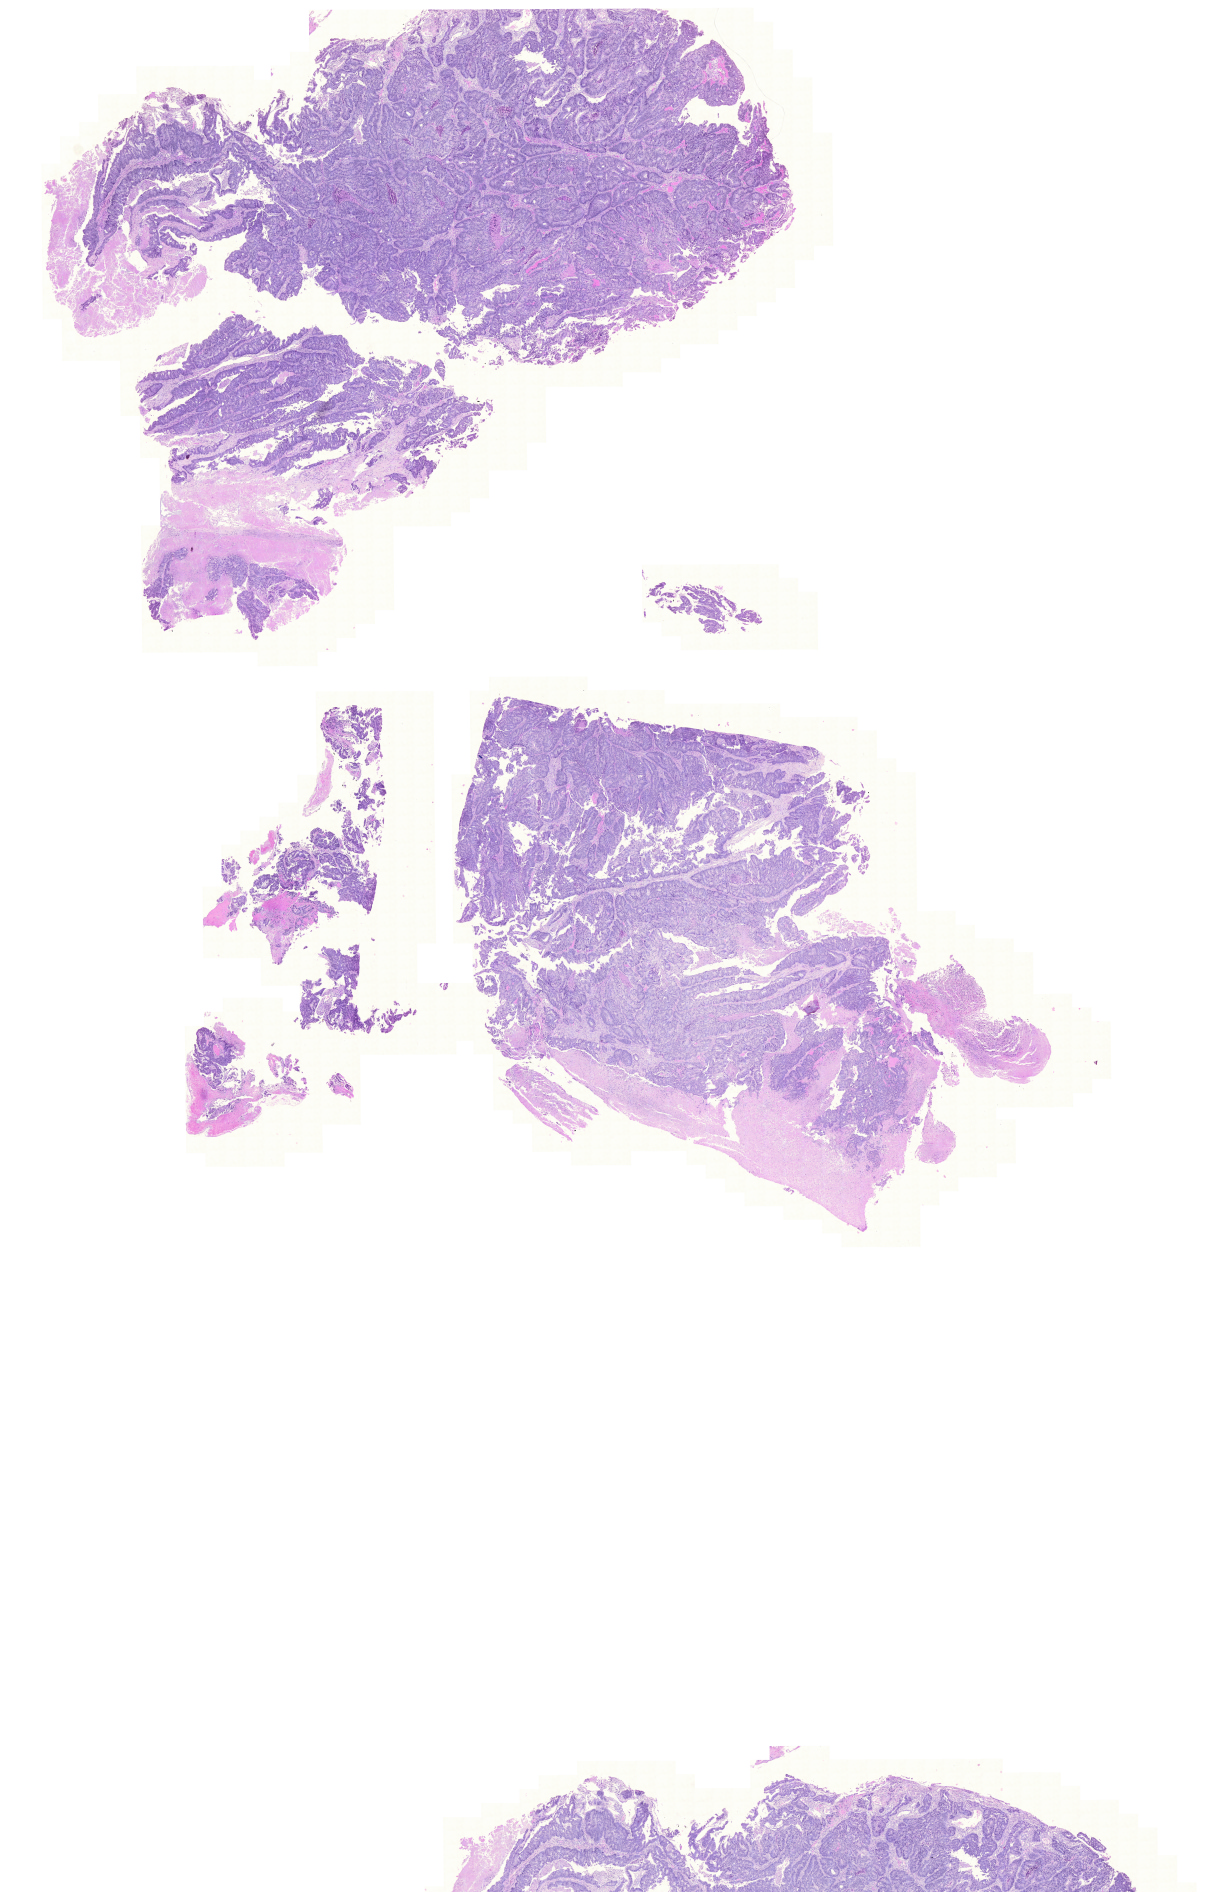
H&E-stained whole-slide image — shown as a low-resolution overview of the whole scanned area (about 18.3 x 28.2 mm, acquisition: 20x scan), formalin-fixed paraffin-embedded (FFPE) diagnostic section, primary tumour sample from the colon. Female, age 68 years at initial diagnosis.
* histologic diagnosis: Carcinoma, NOS
* AJCC pathologic stage: IV (6th edition)